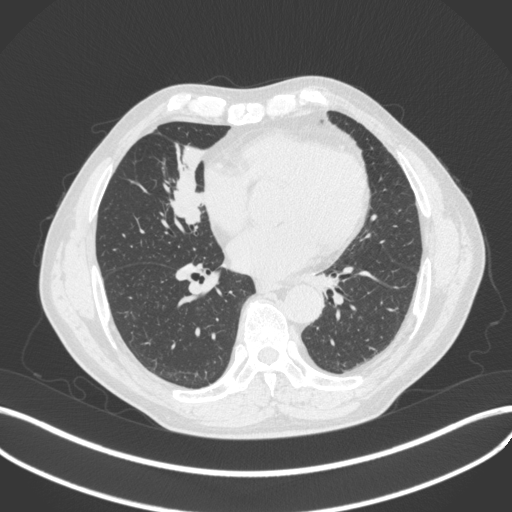
Chest CT, one axial slice. Slice 169 of 429 in the series (ordered by position). Reconstruction kernel B31f. 120 kVp. Lung window (W 1500 / L -600 HU). 1 mm slice thickness. 512 × 512 image matrix, field of view 400 × 400 mm. Male patient, age 61 years. Case-level facts recorded for this patient, not image findings: clinical TNM (as recorded): T2b N1 M0.
Annotated regions visible in this slice (bounding box drawn by a radiologist):
- lung tumour (recorded histology: squamous cell carcinoma): box from (x=157, y=141) to (x=210, y=229) px